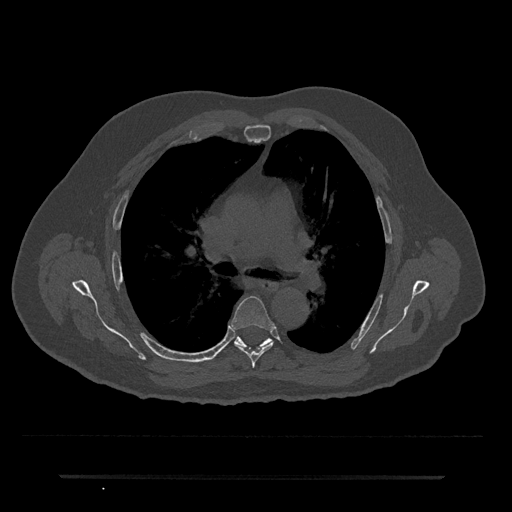
CT including the spine, one axial slice. Position 466 of 797 along the scan axis. Bone window (W 1800 / L 400 HU). 0.5 mm slice thickness. 512 × 512 image matrix. Male patient, age 69 years. Case-level facts recorded for this patient, not image findings: primary cancer: prostate.
Outlined on this slice (semi-automatically segmented with operator editing):
- T5 vertebra: bounding box [x1, y1, x2, y2] px = [231, 296, 275, 368]
- T6 vertebra: [234, 336, 271, 347]